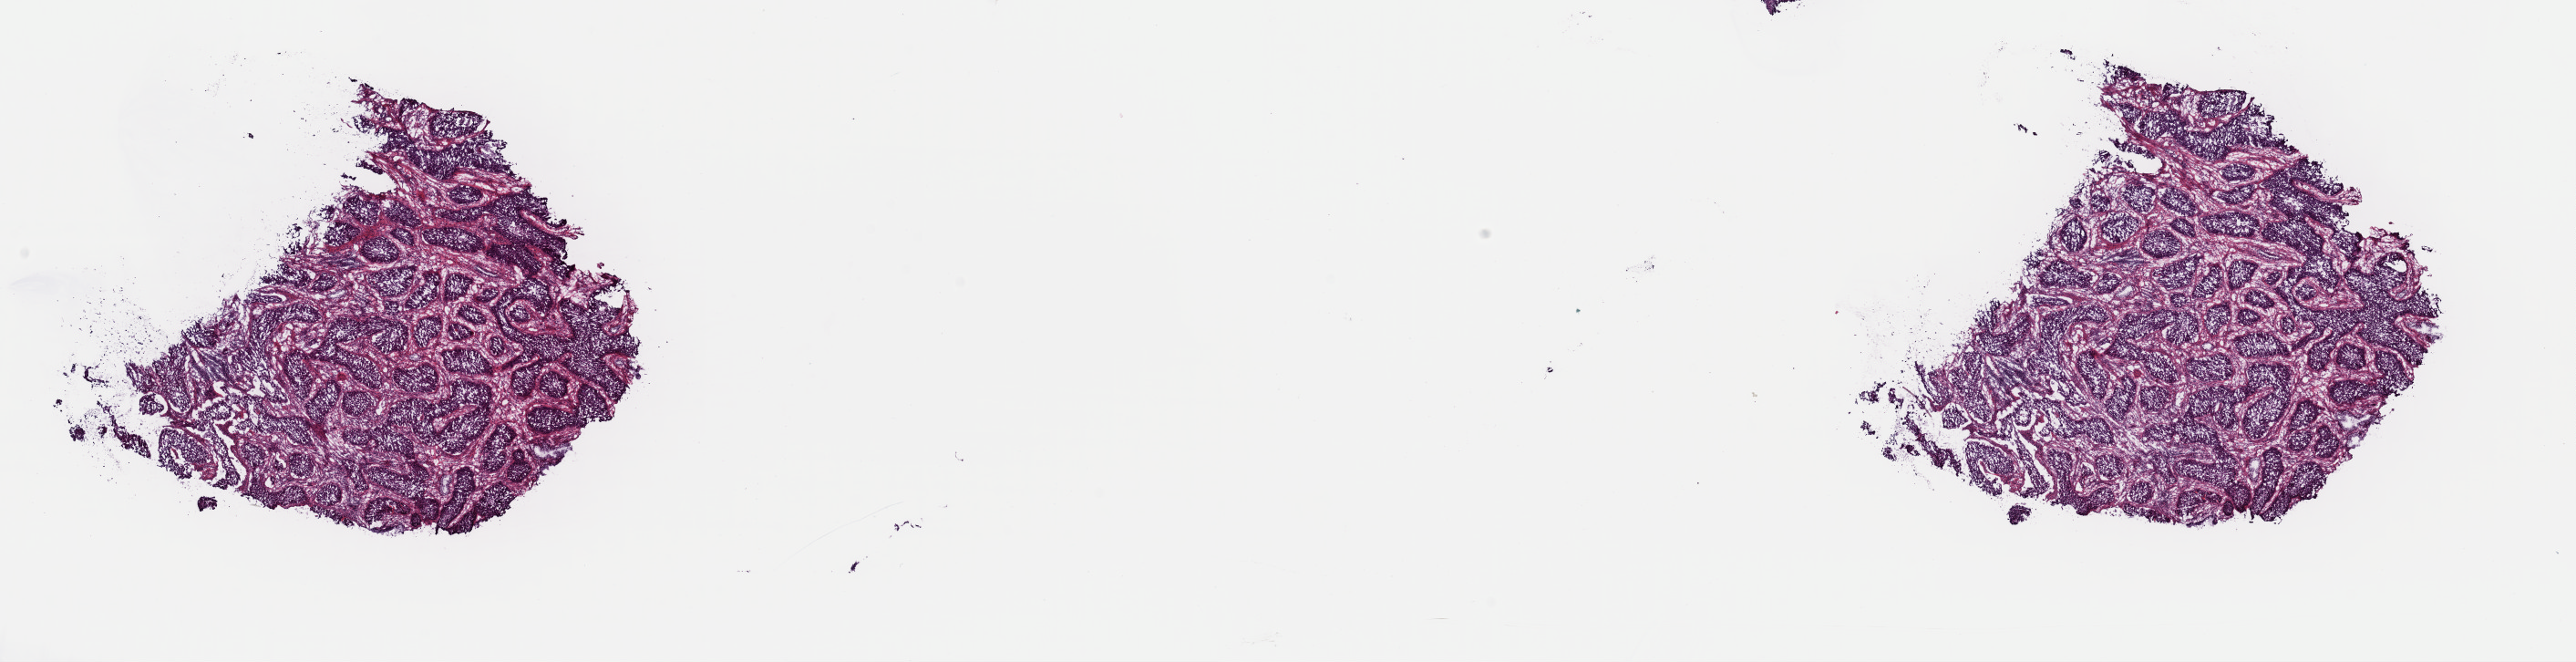
H&E whole-slide image, whole scanned area (about 22.3 x 5.7 mm, slide scanned at 40x) shown as a low-resolution overview, frozen section from the top of the tissue portion, cervix, primary tumour sample. Female patient; age at initial diagnosis 40 years. Histologic grade: G3 (poorly differentiated). Pathologist review of this section (percent, as recorded): tumour cells 100%, tumour nuclei 85%, normal cells 0%, stromal cells 0%, necrosis 0%. Infiltration values recorded for this section: lymphocyte infiltration 5%, monocyte infiltration 0%, neutrophil infiltration 0%.
Pathologic diagnosis: Squamous cell carcinoma, NOS. FIGO stage: IB1.